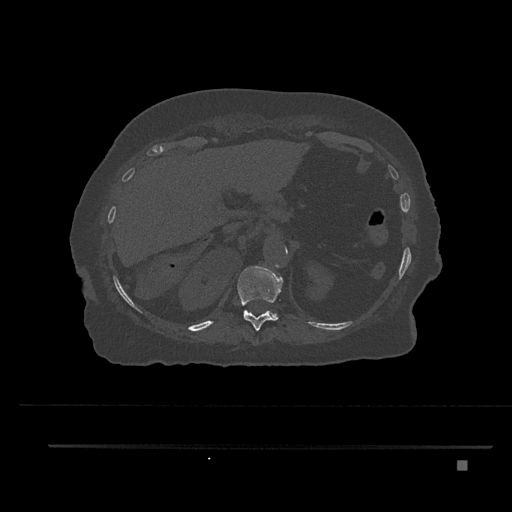
CT including the spine, one axial slice; slice 306 of 797 in the series (ordered by position); 120 kVp; bone window (W 1800 / L 400 HU); 0.5 mm slice thickness; 512 × 512 image matrix. Patient: female, 76 years. Case-level facts recorded for this patient, not image findings: primary cancer: lung.
Structures marked on this image (semi-automatic segmentation, software-assisted and operator-edited):
- T11 vertebra: bounding box (x1, y1, x2, y2) in pixels: (237, 266, 283, 331)
- T12 vertebra: (263, 312, 277, 317)